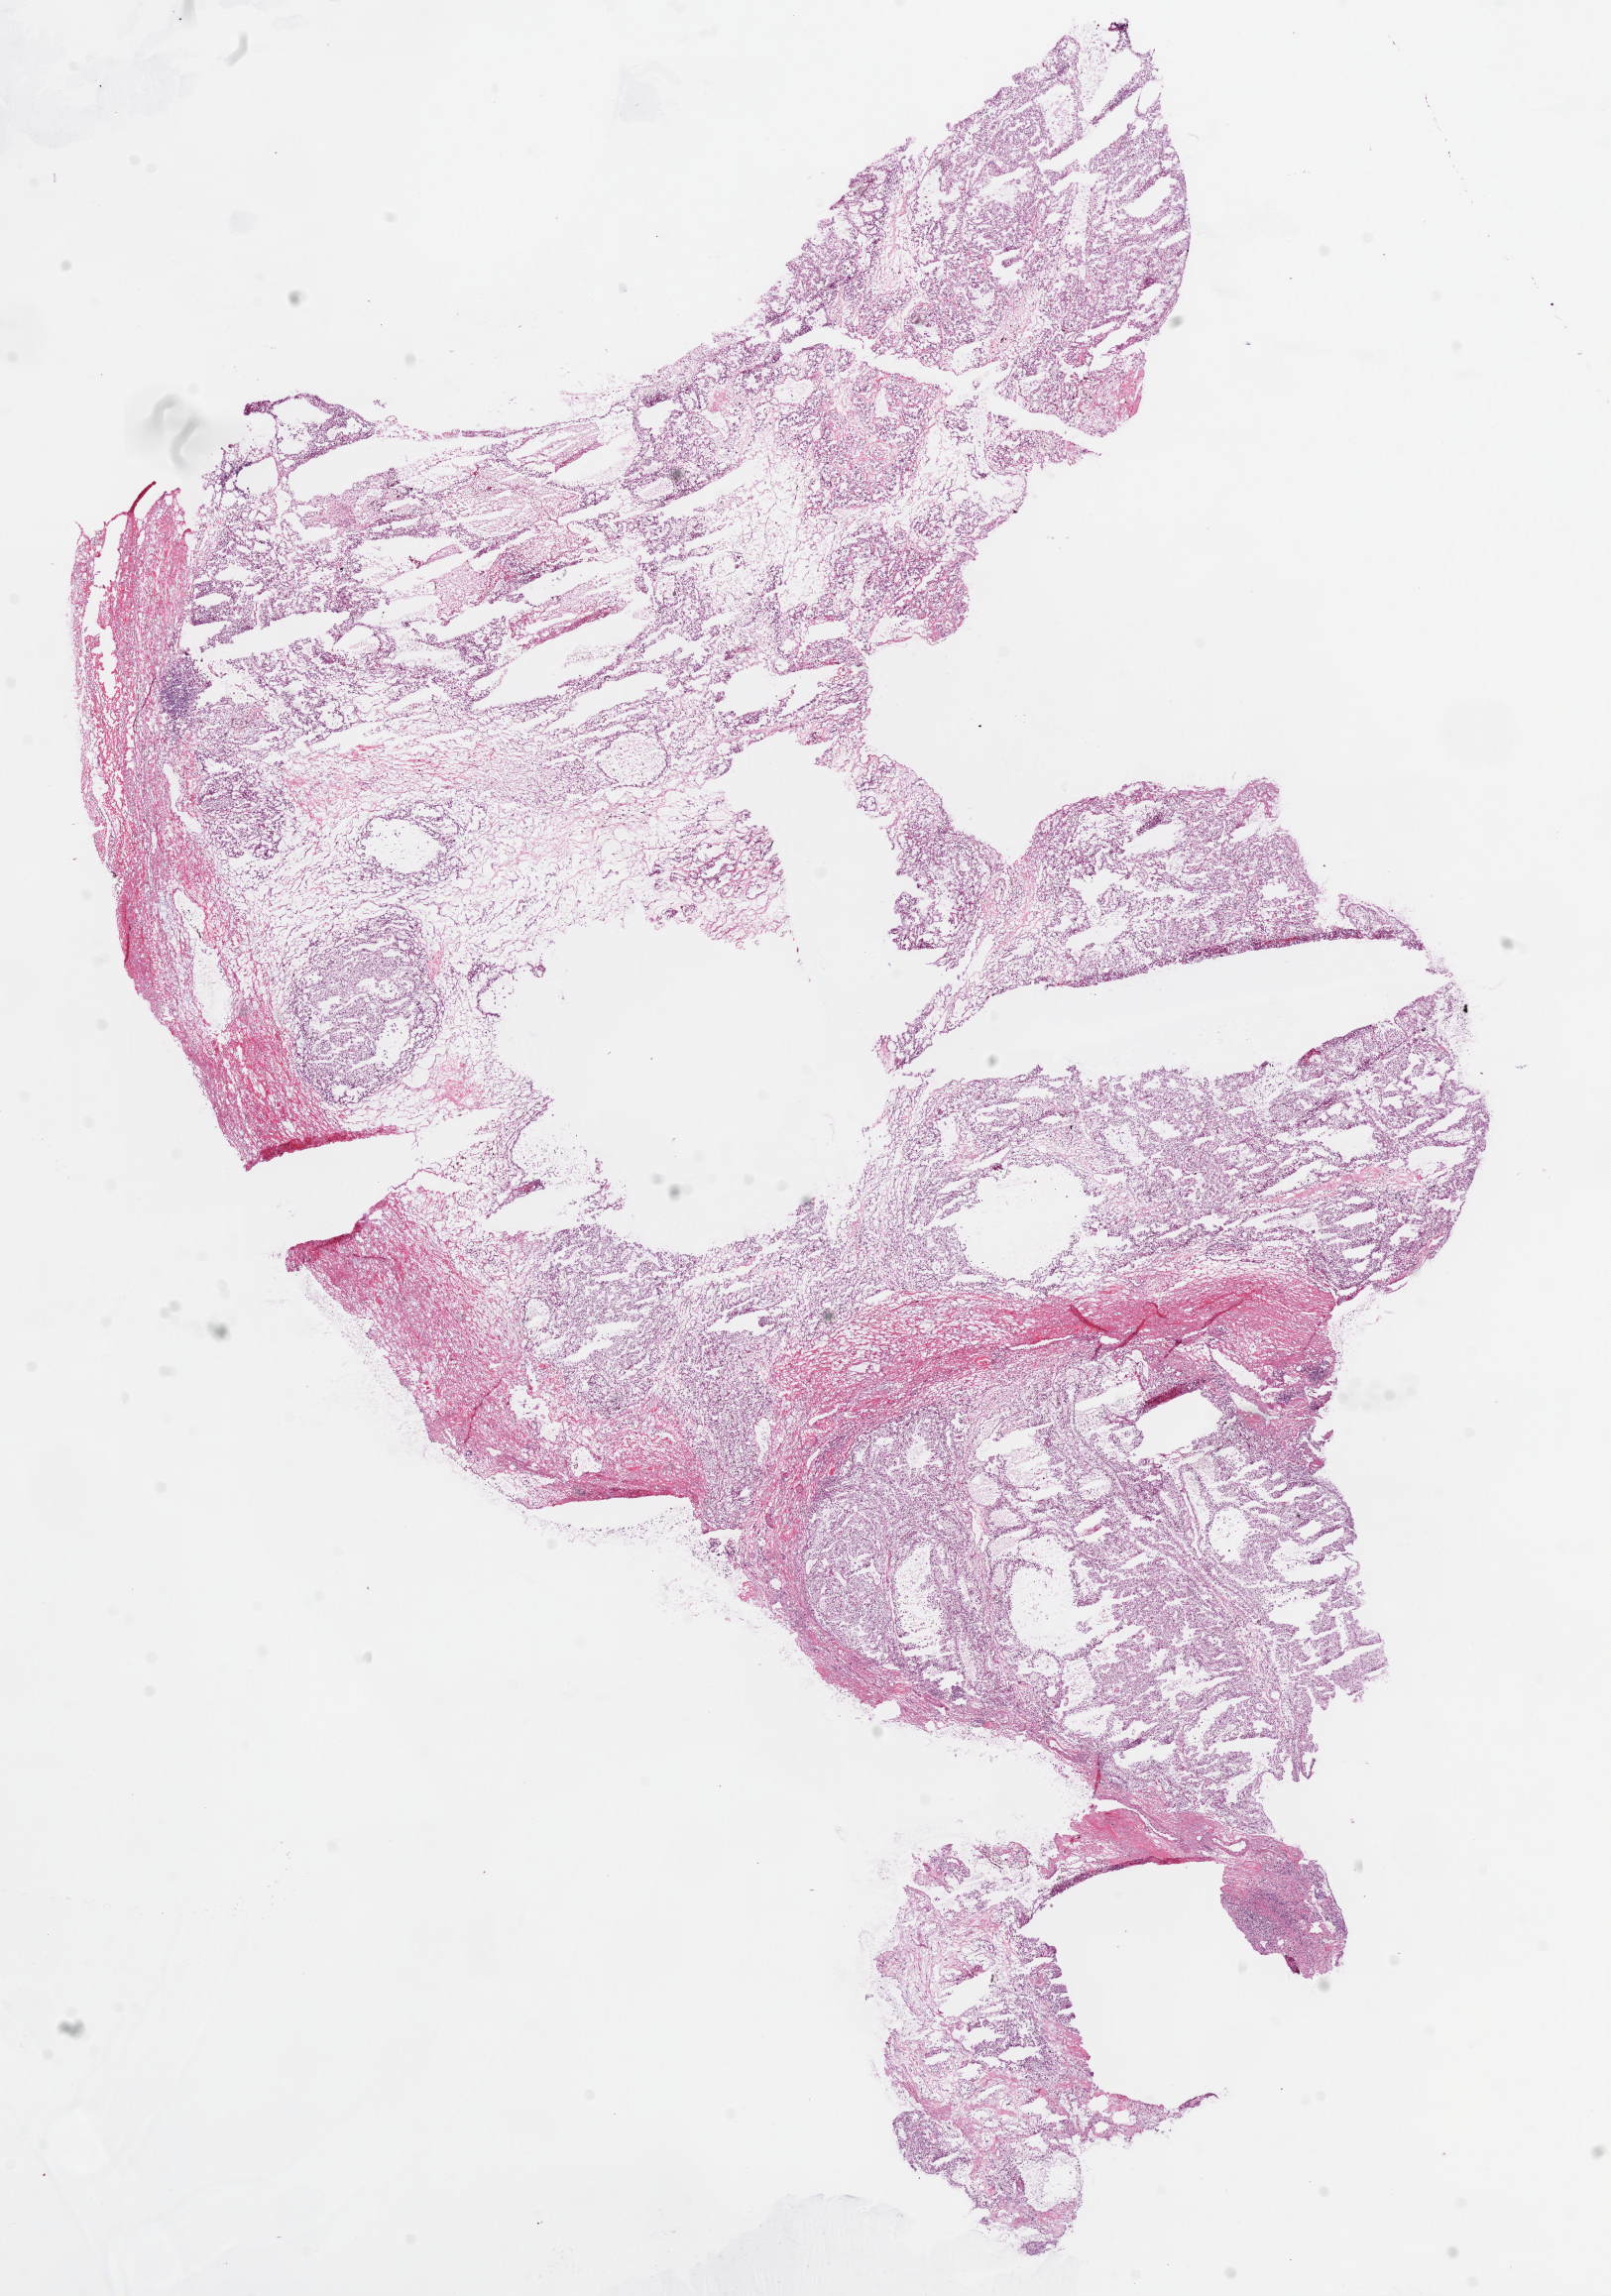
H&E whole-slide image — shown as a low-resolution overview of the whole scanned area (about 13.0 x 18.6 mm). Frozen section. Primary tumour sample from the kidney. Male patient; age at initial diagnosis 67 years. Histologic grade: G2 (moderately differentiated). Composition of this section per pathologist review: tumour cells 85%, tumour nuclei 80%, normal cells 0%, stromal cells 15%, necrosis 0%.
* diagnosis: Clear cell adenocarcinoma, NOS
* laterality: left
* lymph nodes positive (case pathology): 0 of 3 examined
* TNM: T3a N0 M0
* AJCC pathologic stage: III